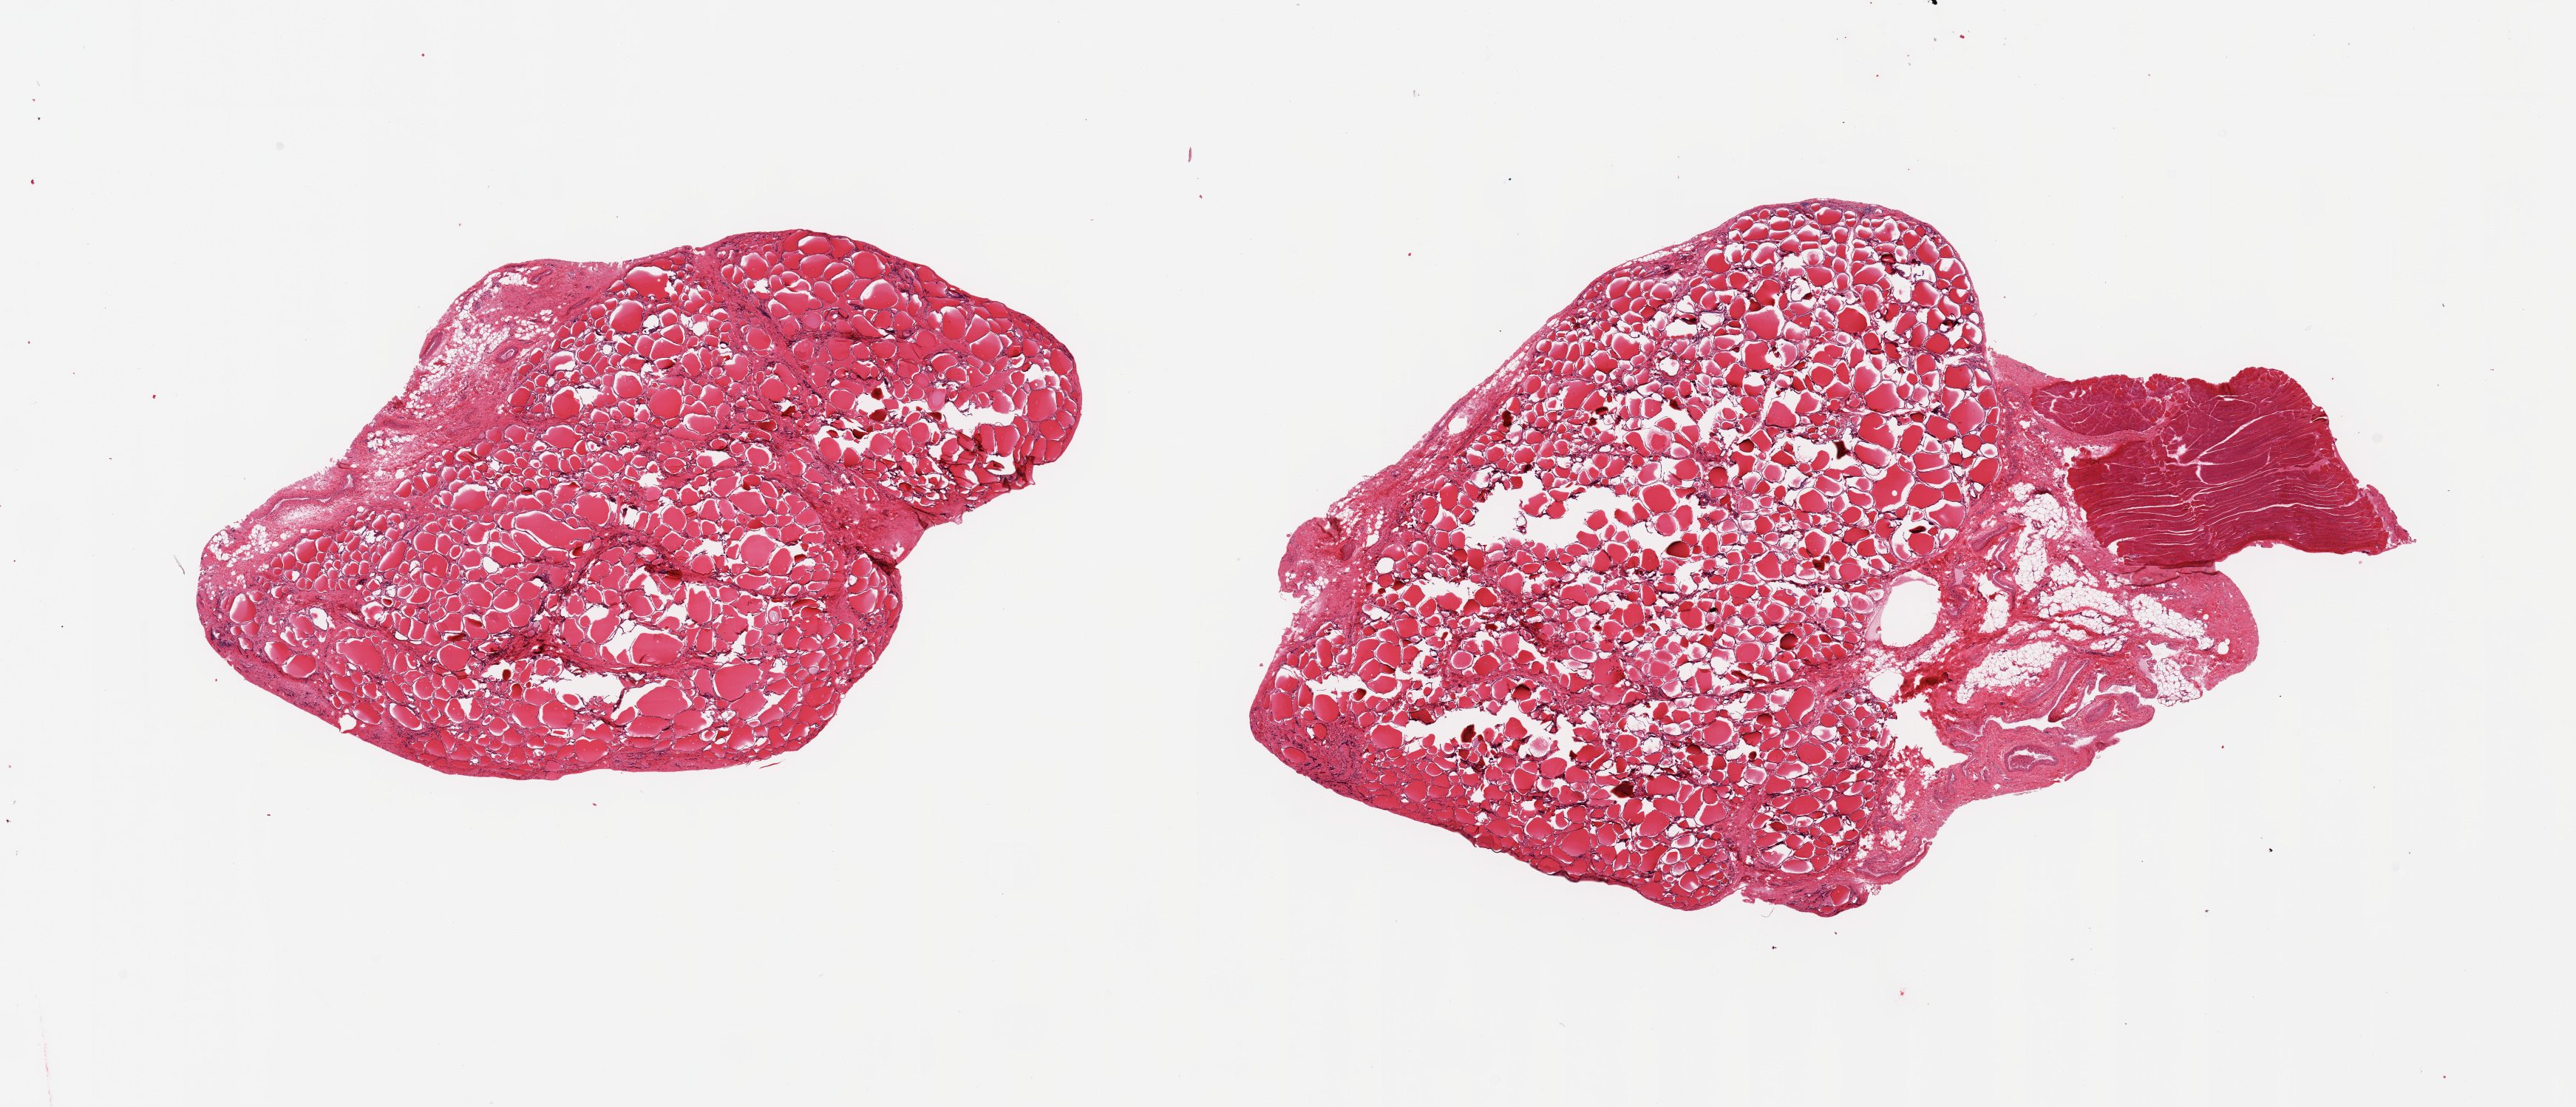
Whole-slide image, haematoxylin and eosin stain, whole scanned area (about 27.6 x 11.8 mm) shown as a low-resolution overview. PAXgene-fixed, paraffin-embedded tissue. Target tissue: thyroid. Tissue donor sample. Donor: male.
- reviewer comment on this tissue sample: 2 pieces; one piece includes ~10% fat/fibrous/vascular tissue, second includes ~30% fat/vascular/skeletal muscle (contaminating elements marked)